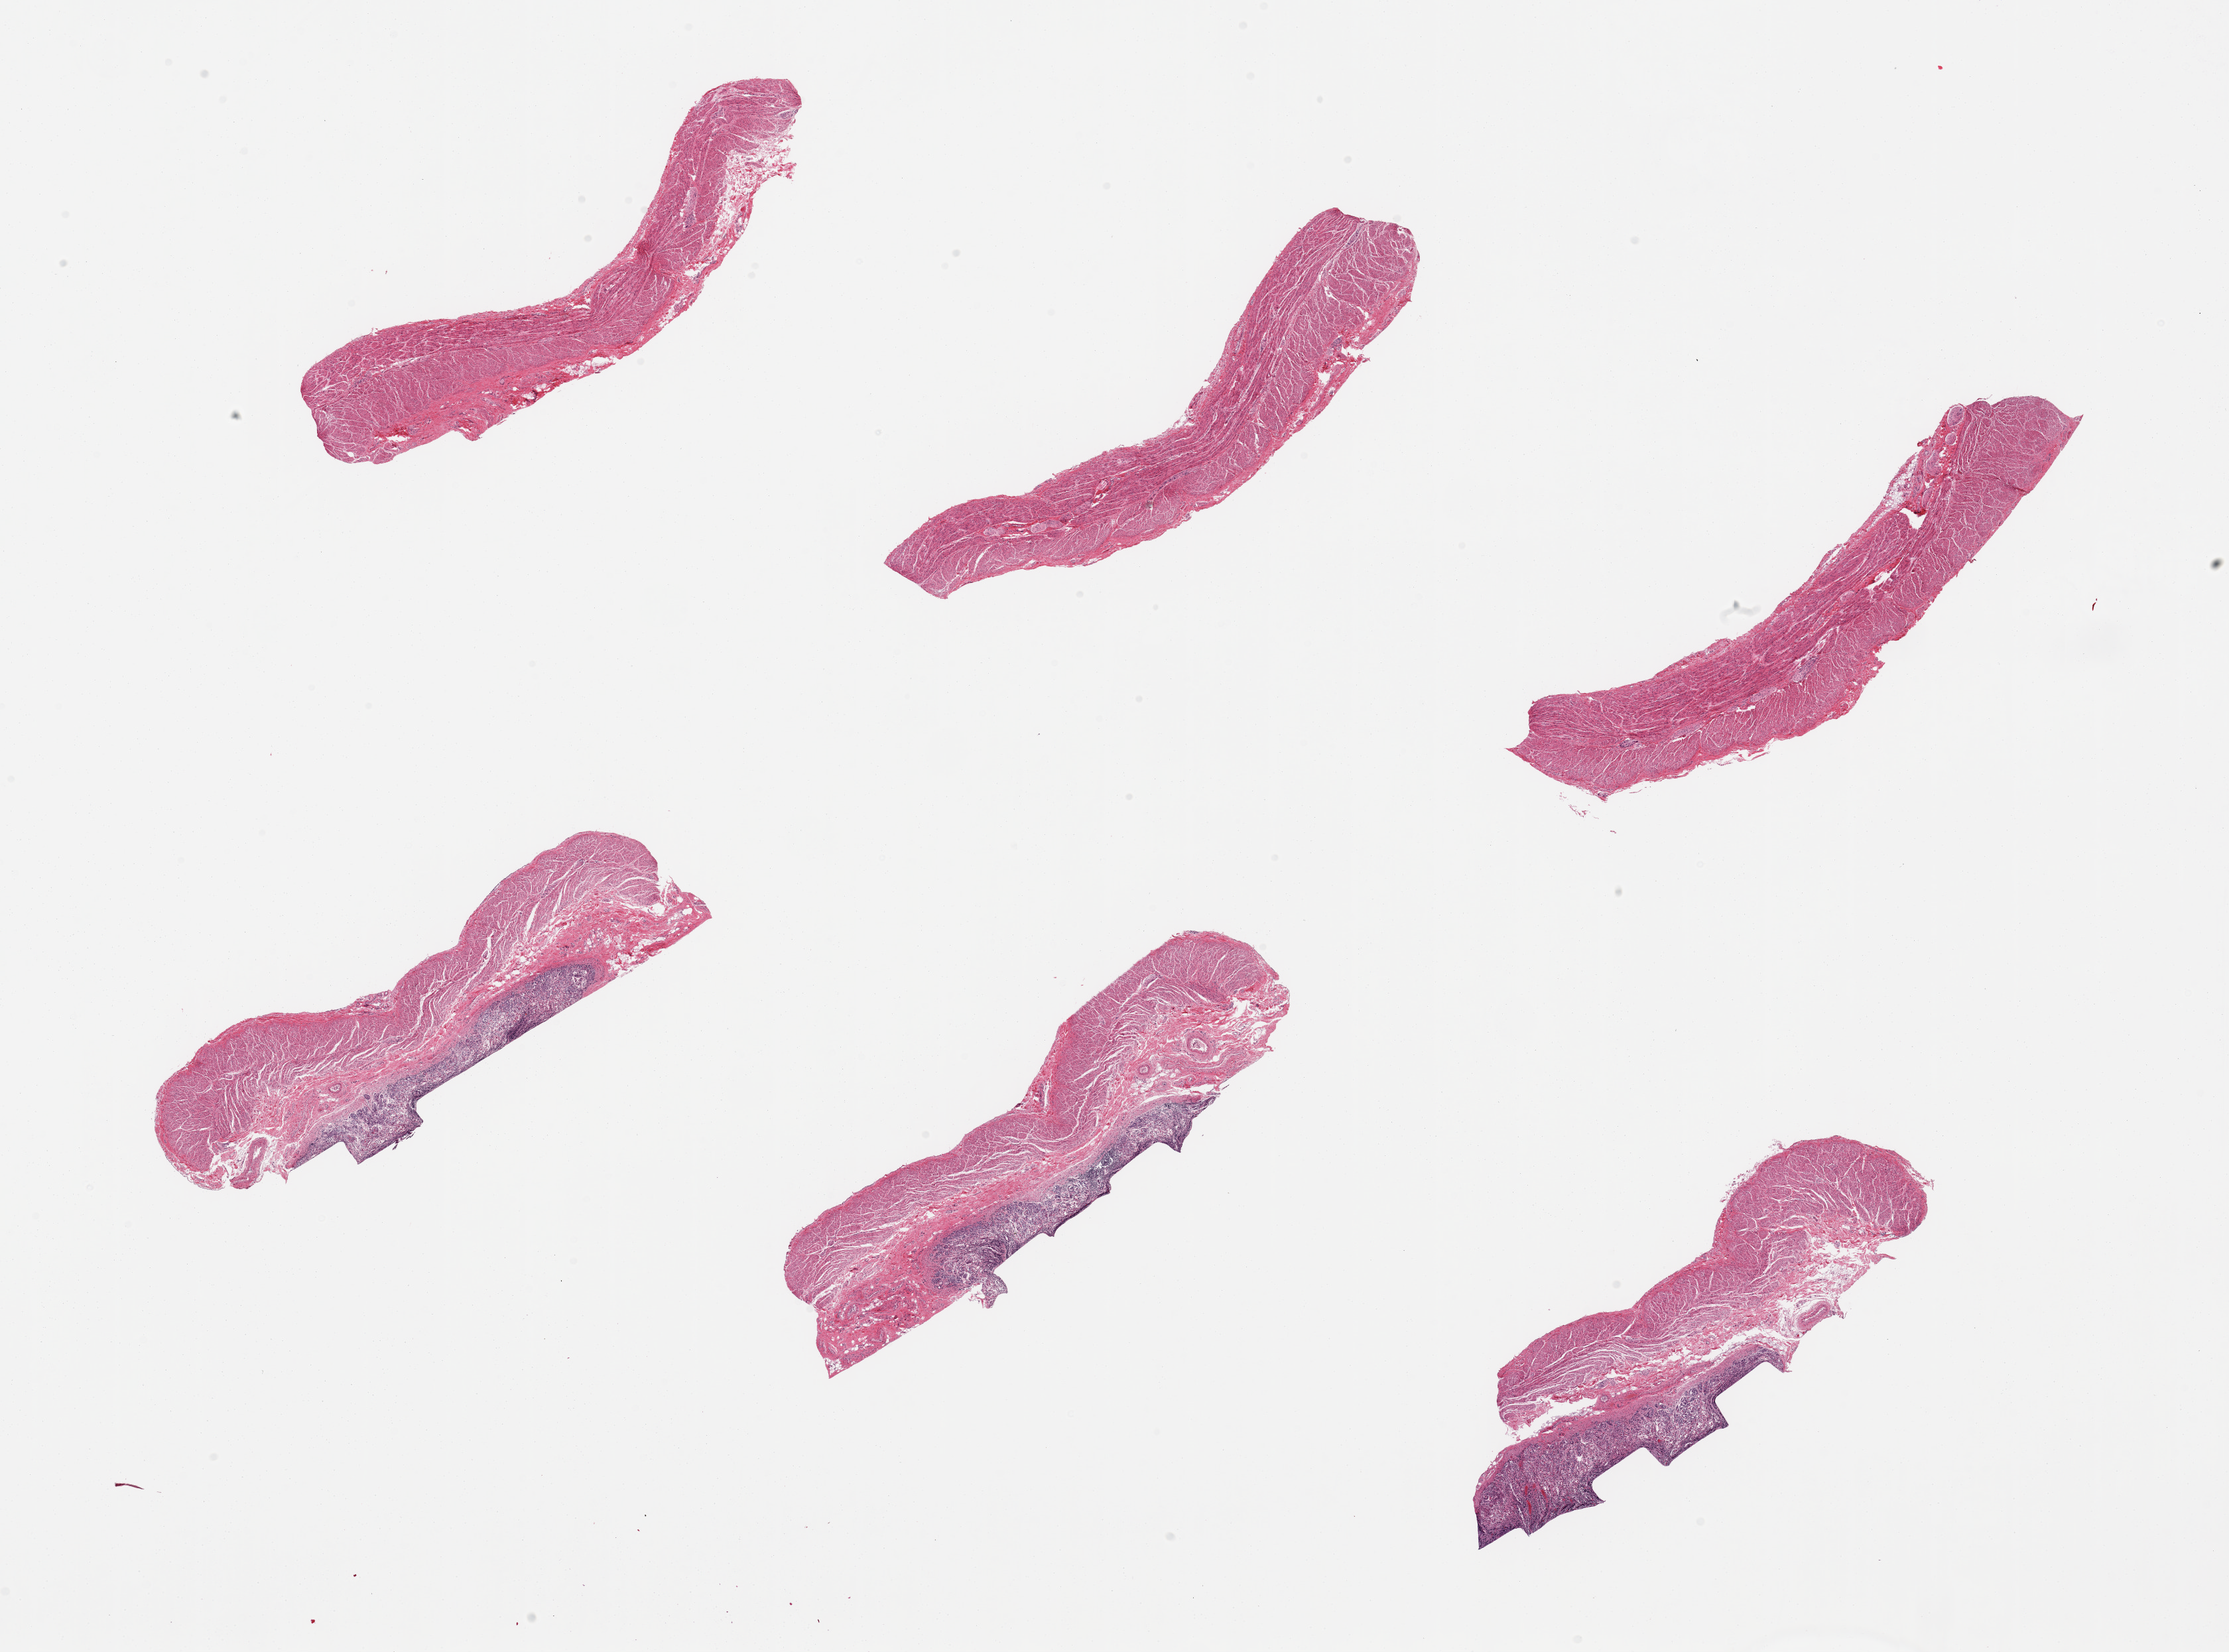
Whole-slide image, hematoxylin and eosin (H&E) stain, brightfield, low-resolution overview of the scanned area, about 26.6 x 19.7 mm (from a 20x scan). PAXgene-fixed, paraffin-embedded tissue. Target tissue: gastroesophageal junction. Tissue donor sample. Donor sex: male.
Review note (as recorded): 6 pieces; 3 pieces have autolyzed gastric fundic mucosa with chronic gastritis; likely represents gastric mucosa in a hiatus hernia rather than glandular metaplasia or sampling error.